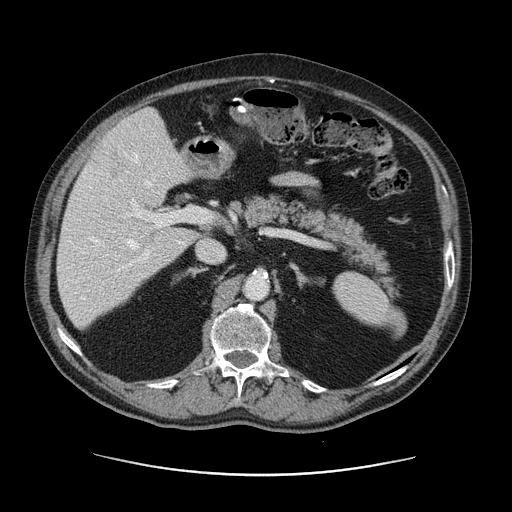
Contrast-enhanced abdominal CT, one axial slice. Slice 72 of 141 in the series (ordered by position). 120 kVp. Intravenous contrast given. Soft-tissue window (W 400 / L 40 HU). 2.5 mm slice thickness. 512 × 512 image matrix, field of view 395 × 395 mm. Male patient, age 72 years. From the clinical record (not read from this slice): diagnosis: colorectal cancer liver metastases, imaged before liver resection; multiple liver metastases: yes.
Structures marked on this image (outlined manually by an expert reader):
- hepatic veins: bounding box <89,154,150,249> (left, top, right, bottom; pixels)
- liver: <57,109,198,328>
- planned liver remnant (the part of the liver to remain after resection): <58,178,198,328>
- portal vein (with intrahepatic branches): <81,199,203,300>
- liver metastasis: <110,170,118,176>